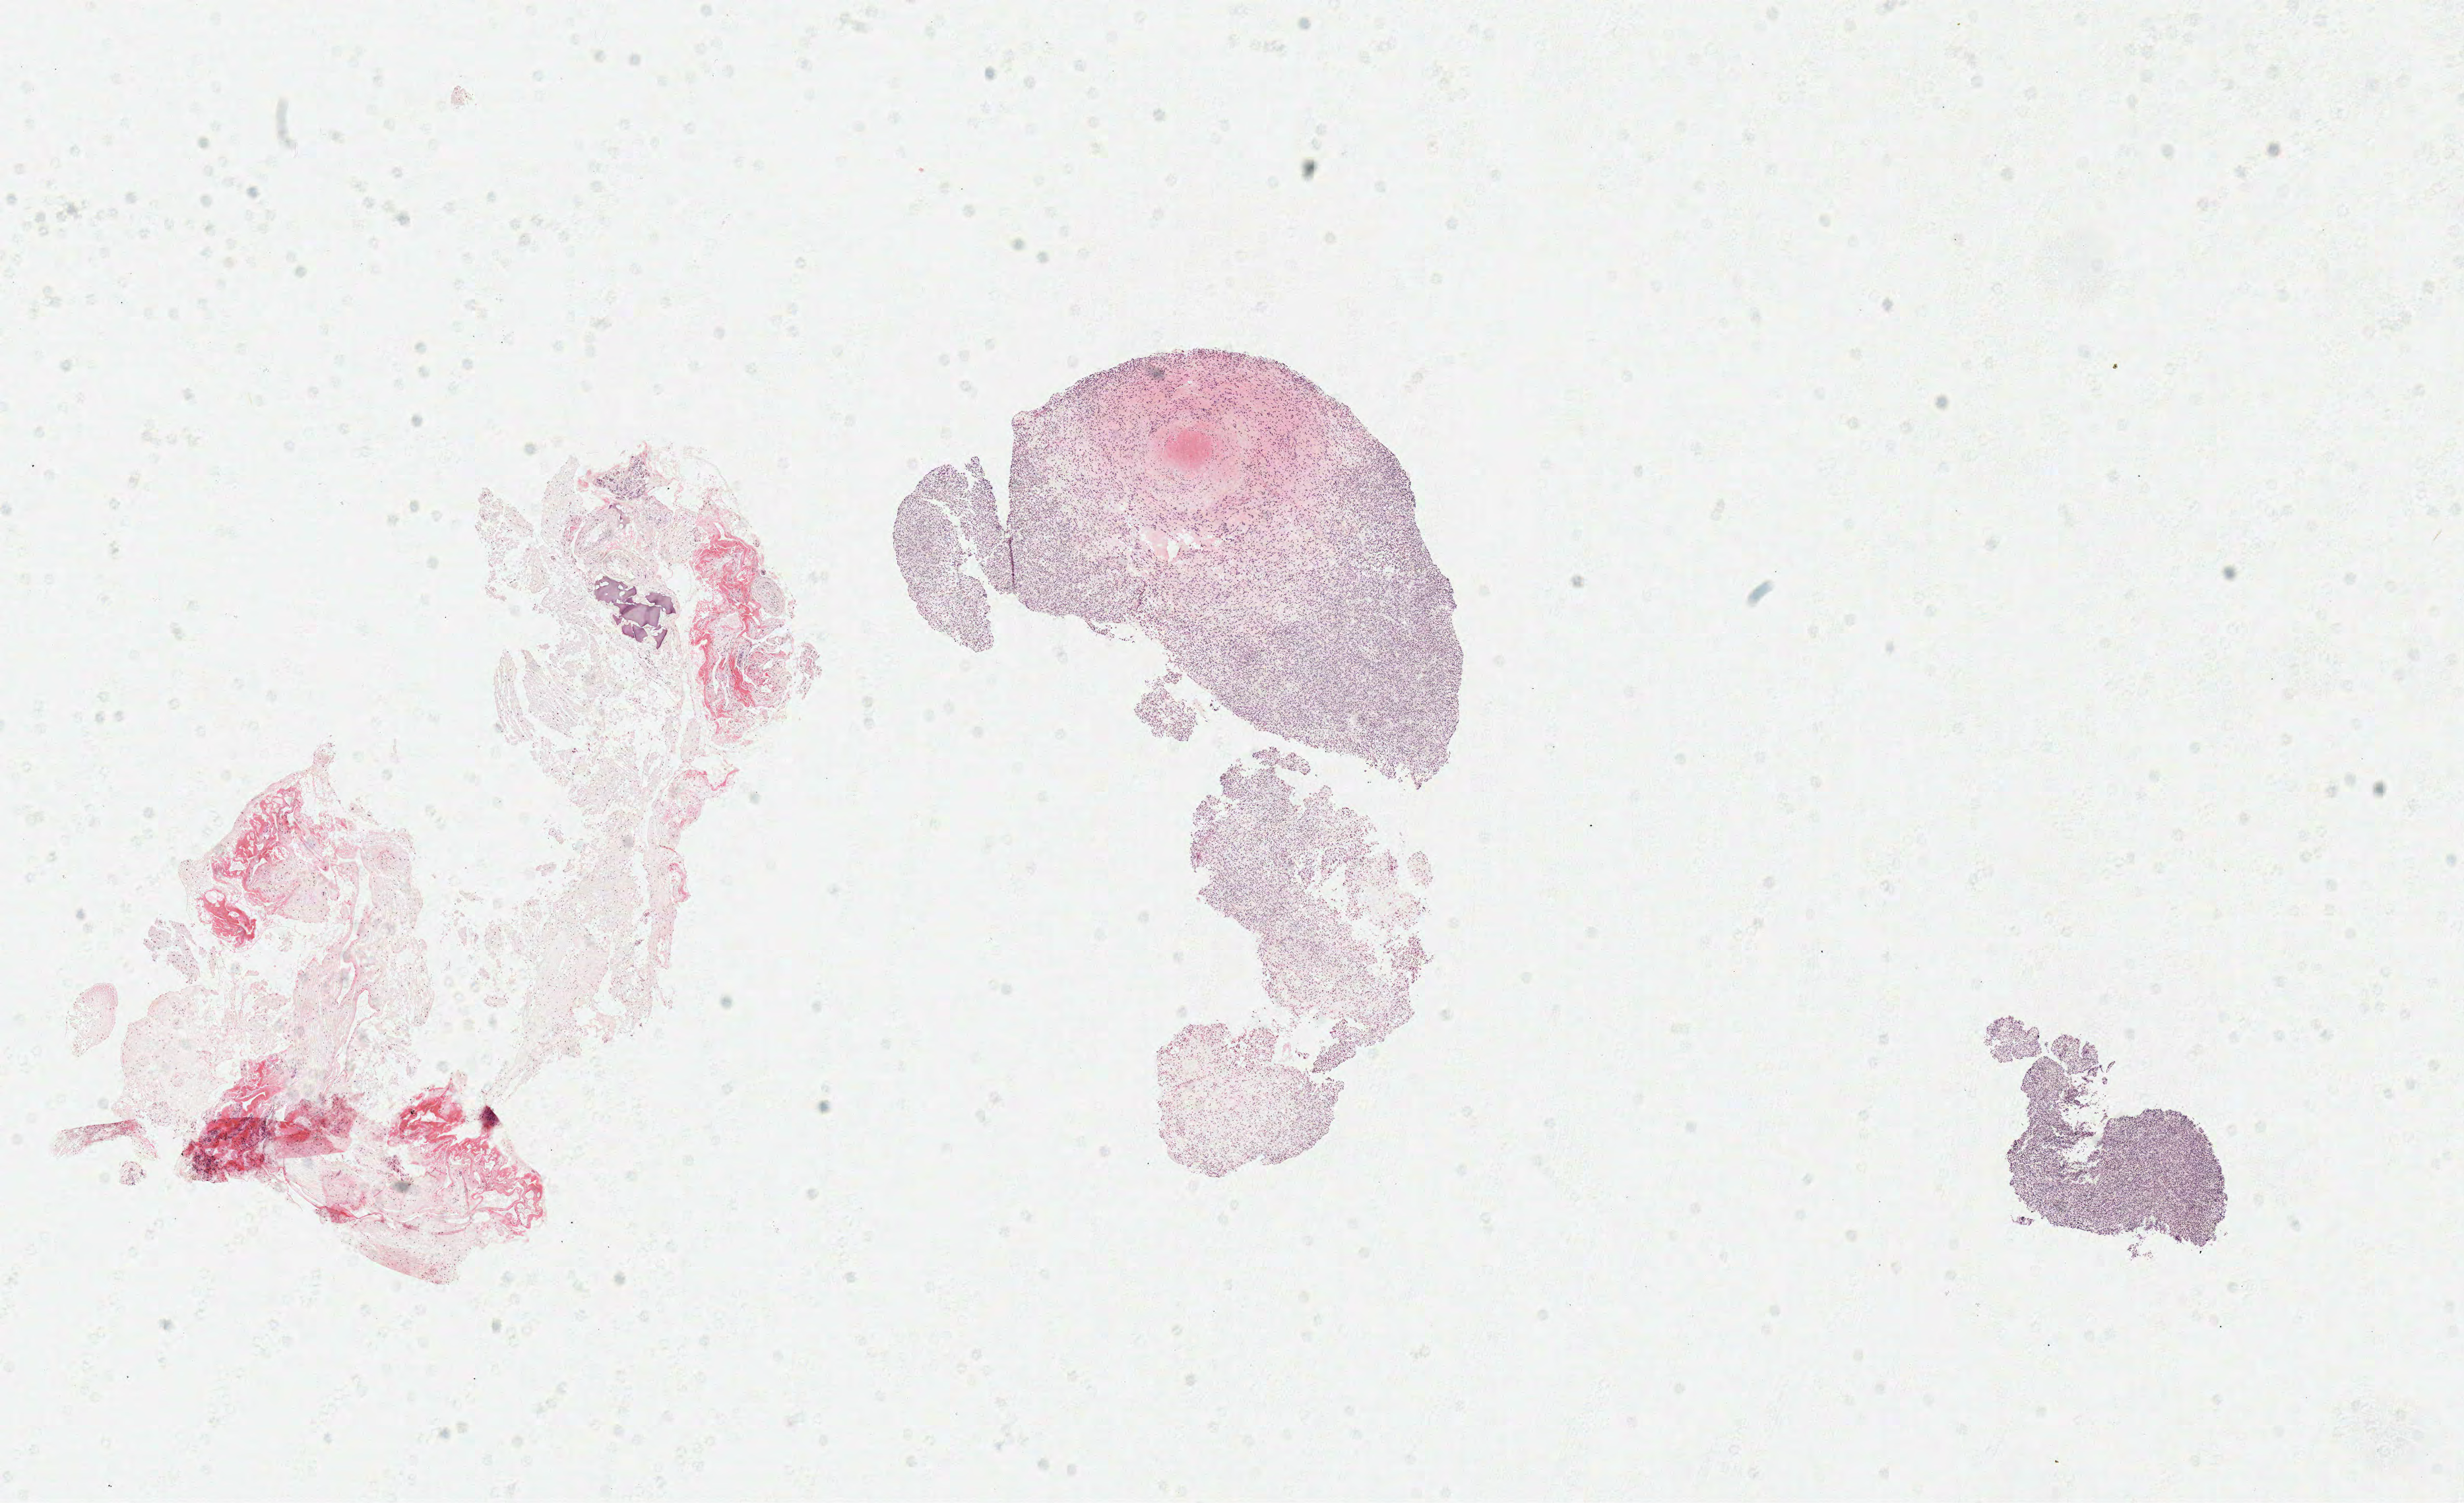
Digitized H&E tissue section (whole slide) — low-resolution overview of the scanned area, about 14.7 x 9.0 mm (acquisition: 40x scan), formalin-fixed paraffin-embedded (FFPE) diagnostic section, sample: primary tumour, brain. Patient: male, age at initial diagnosis 51 years.
Histologic diagnosis: Glioblastoma.